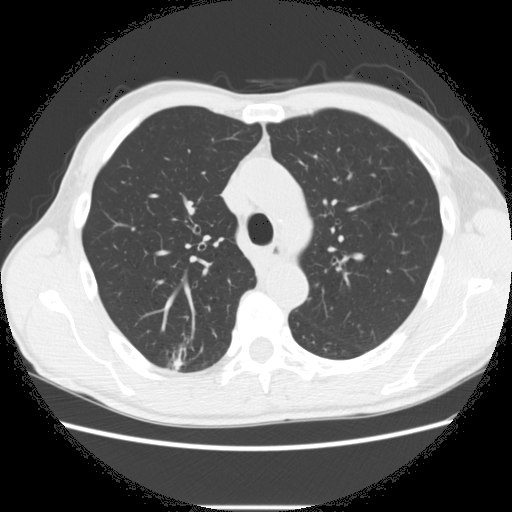
Low-dose screening chest CT, one axial slice; reconstruction kernel STANDARD; lung window (W 1500 / L -600 HU); 2.5 mm slice thickness; 512 × 512 image matrix.
Outlined on this slice (expert manual segmentation):
- lesion 1 (tumor, upper lobe of right lung): box from (x=172, y=358) to (x=183, y=370) px